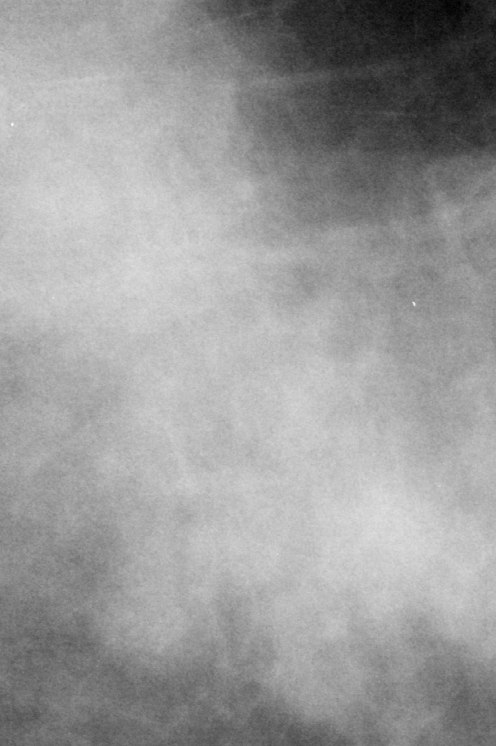
Cropped region of a digitized screen-film mammogram centred on a radiologist-marked abnormality; left breast; CC view; BI-RADS breast density category 3 (scale 1–4).
Mass, shape focal asymmetric density; BI-RADS assessment category 2; benign without callback (not worked up further).